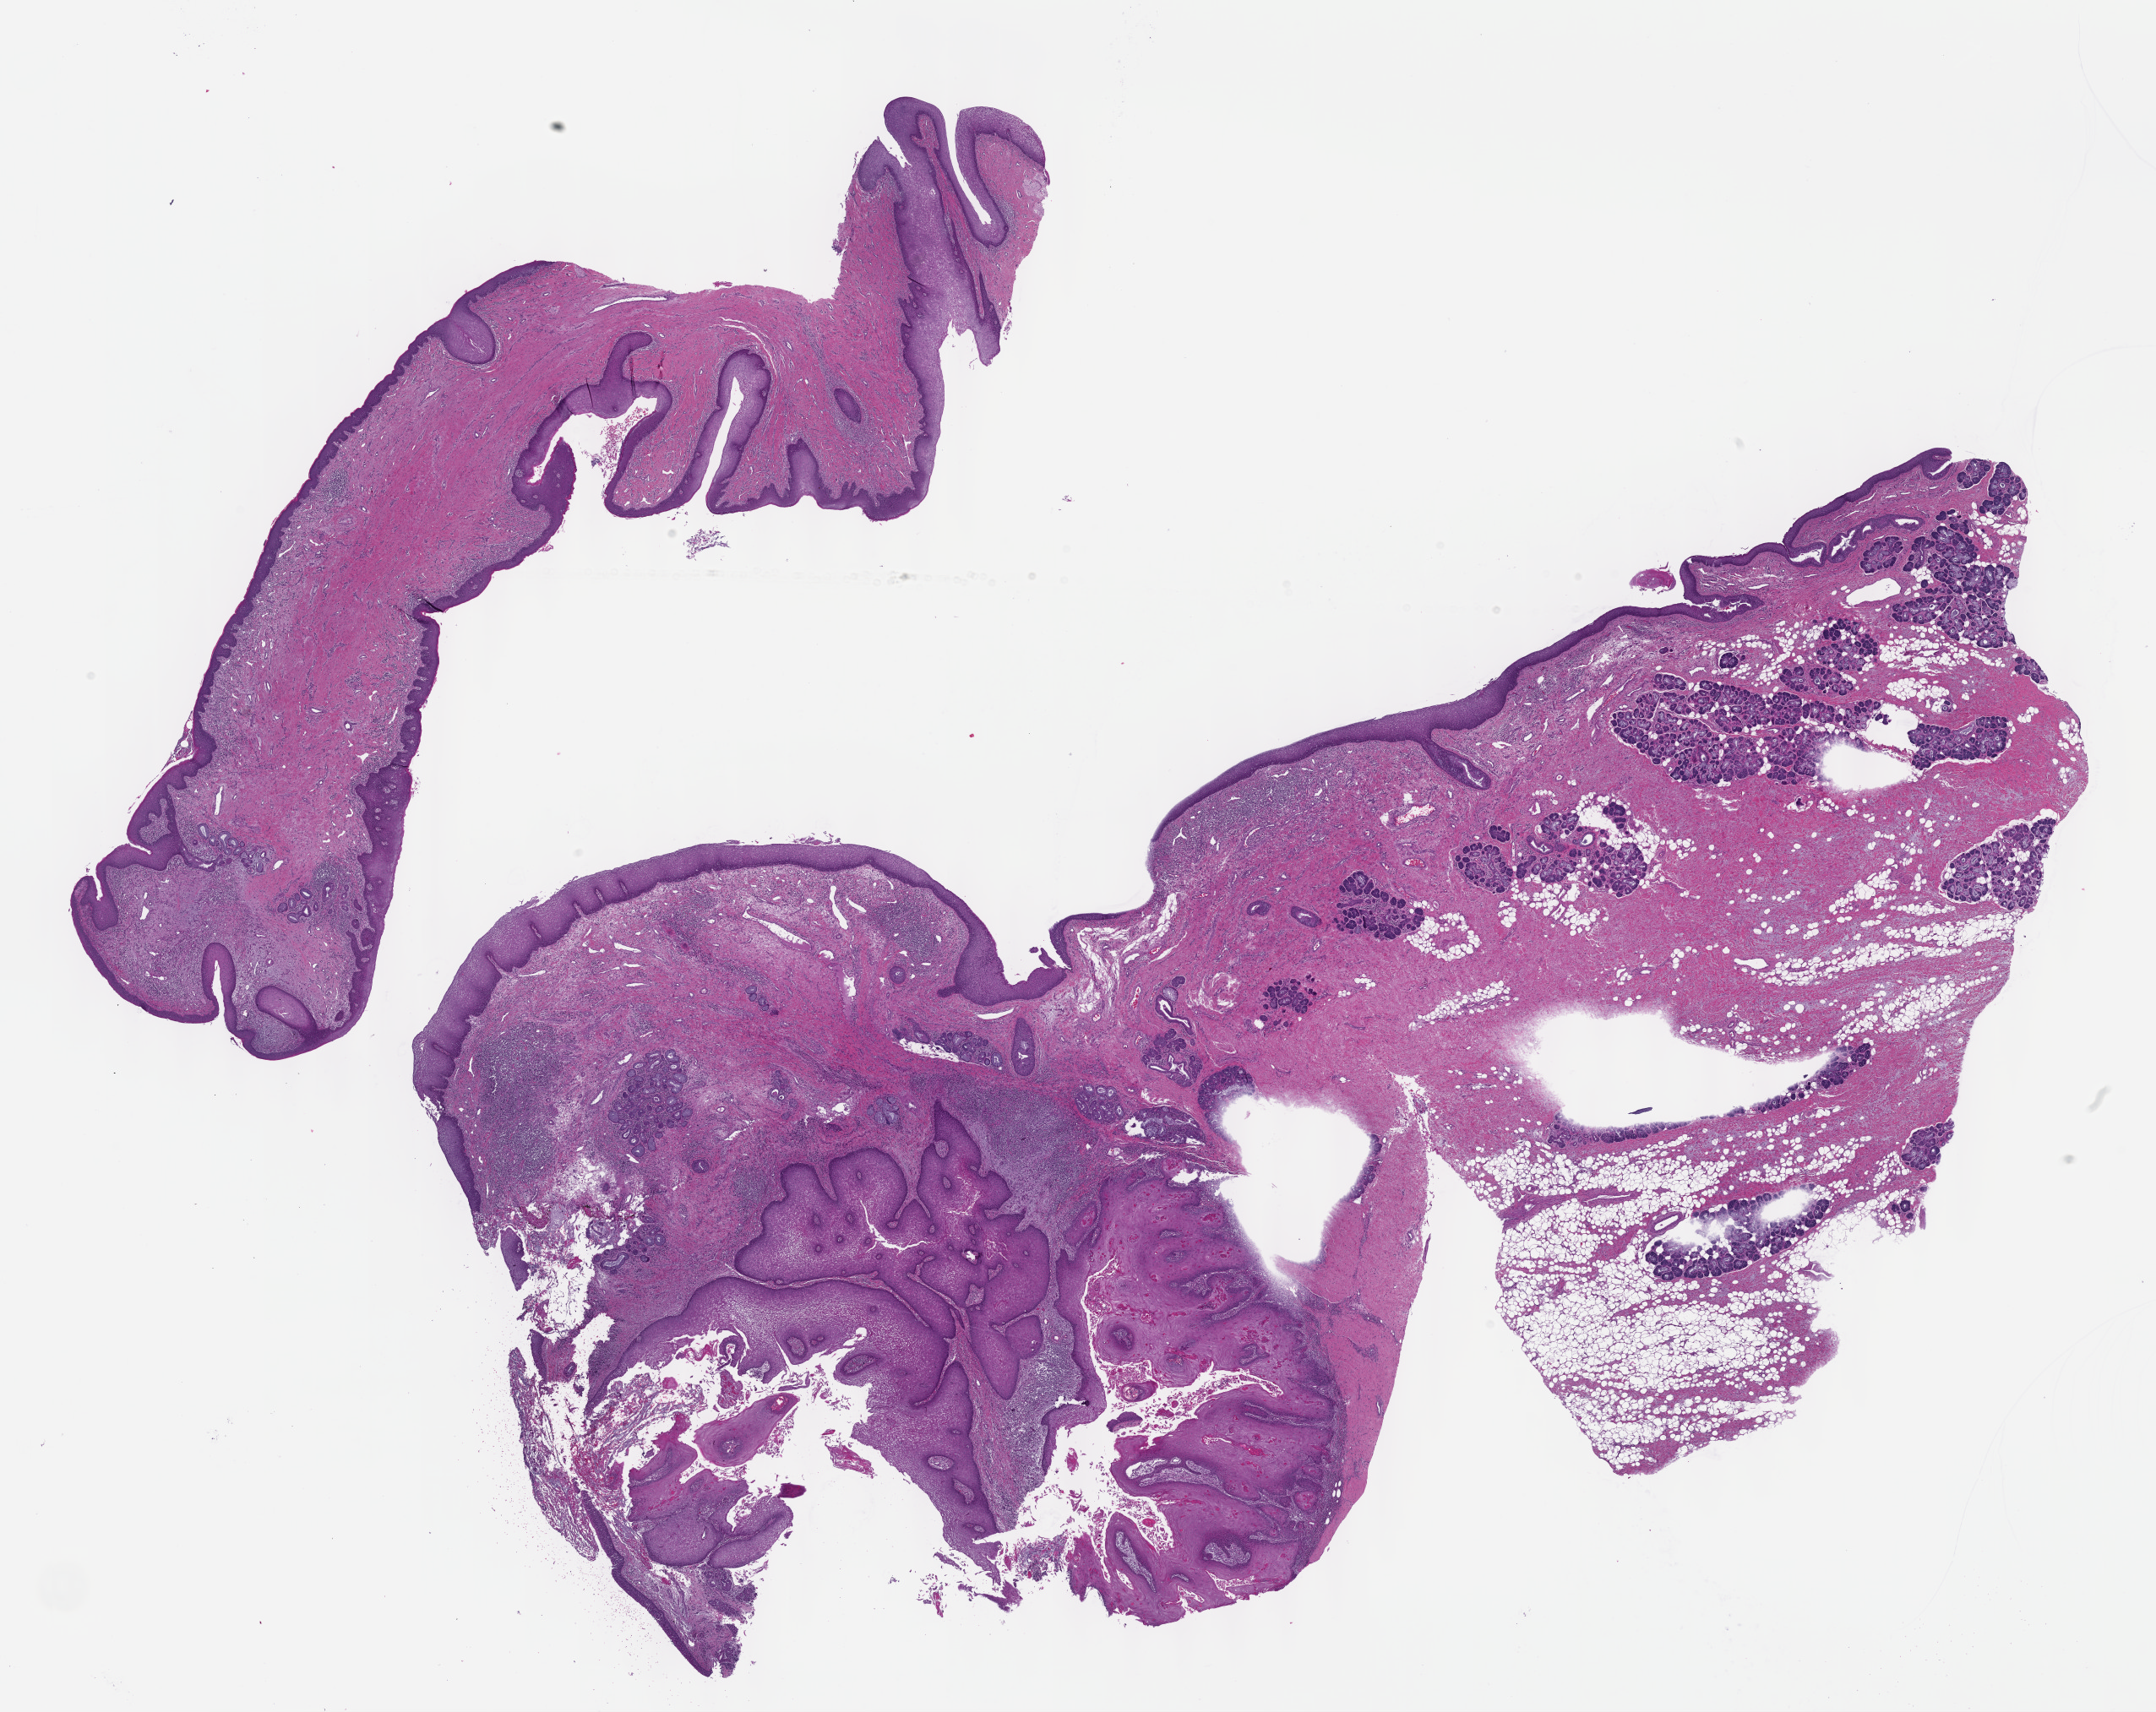
Hematoxylin and eosin (H&E) stained whole-slide image, shown as a low-resolution overview of the whole scanned area (about 20.6 x 16.4 mm, from a 40x scan), formalin-fixed paraffin-embedded (FFPE) diagnostic section, sample: primary tumour, head and neck. Male, age 52 years at initial diagnosis.
Histologic diagnosis: Squamous cell carcinoma, NOS (overlapping lesion of lip, oral cavity and pharynx).